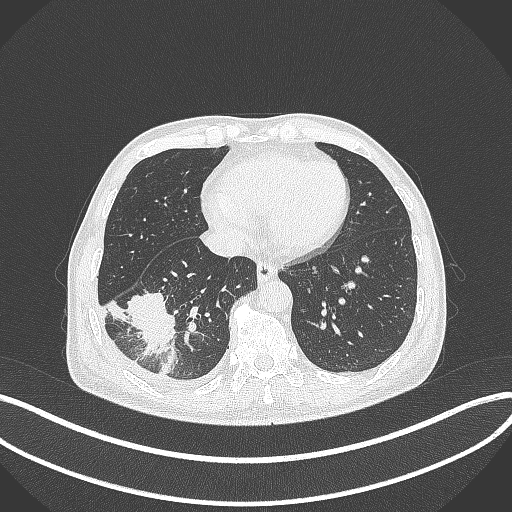
Chest CT, one axial slice. Slice 118 of 388 in the series (ordered by position). Lung window (W 1500 / L -600 HU). 1 mm slice thickness. 512 × 512 image matrix, field of view 400 × 400 mm. Patient: male, 64 years. Case-level facts recorded for this patient, not image findings: clinical TNM (as recorded): T3 N0 M0; histopathological grade: G2-3.
Outlined on this slice (bounding box drawn by a radiologist):
- lung tumour (recorded histology: adenocarcinoma): bounding box <129,285,176,361> (left, top, right, bottom; pixels)